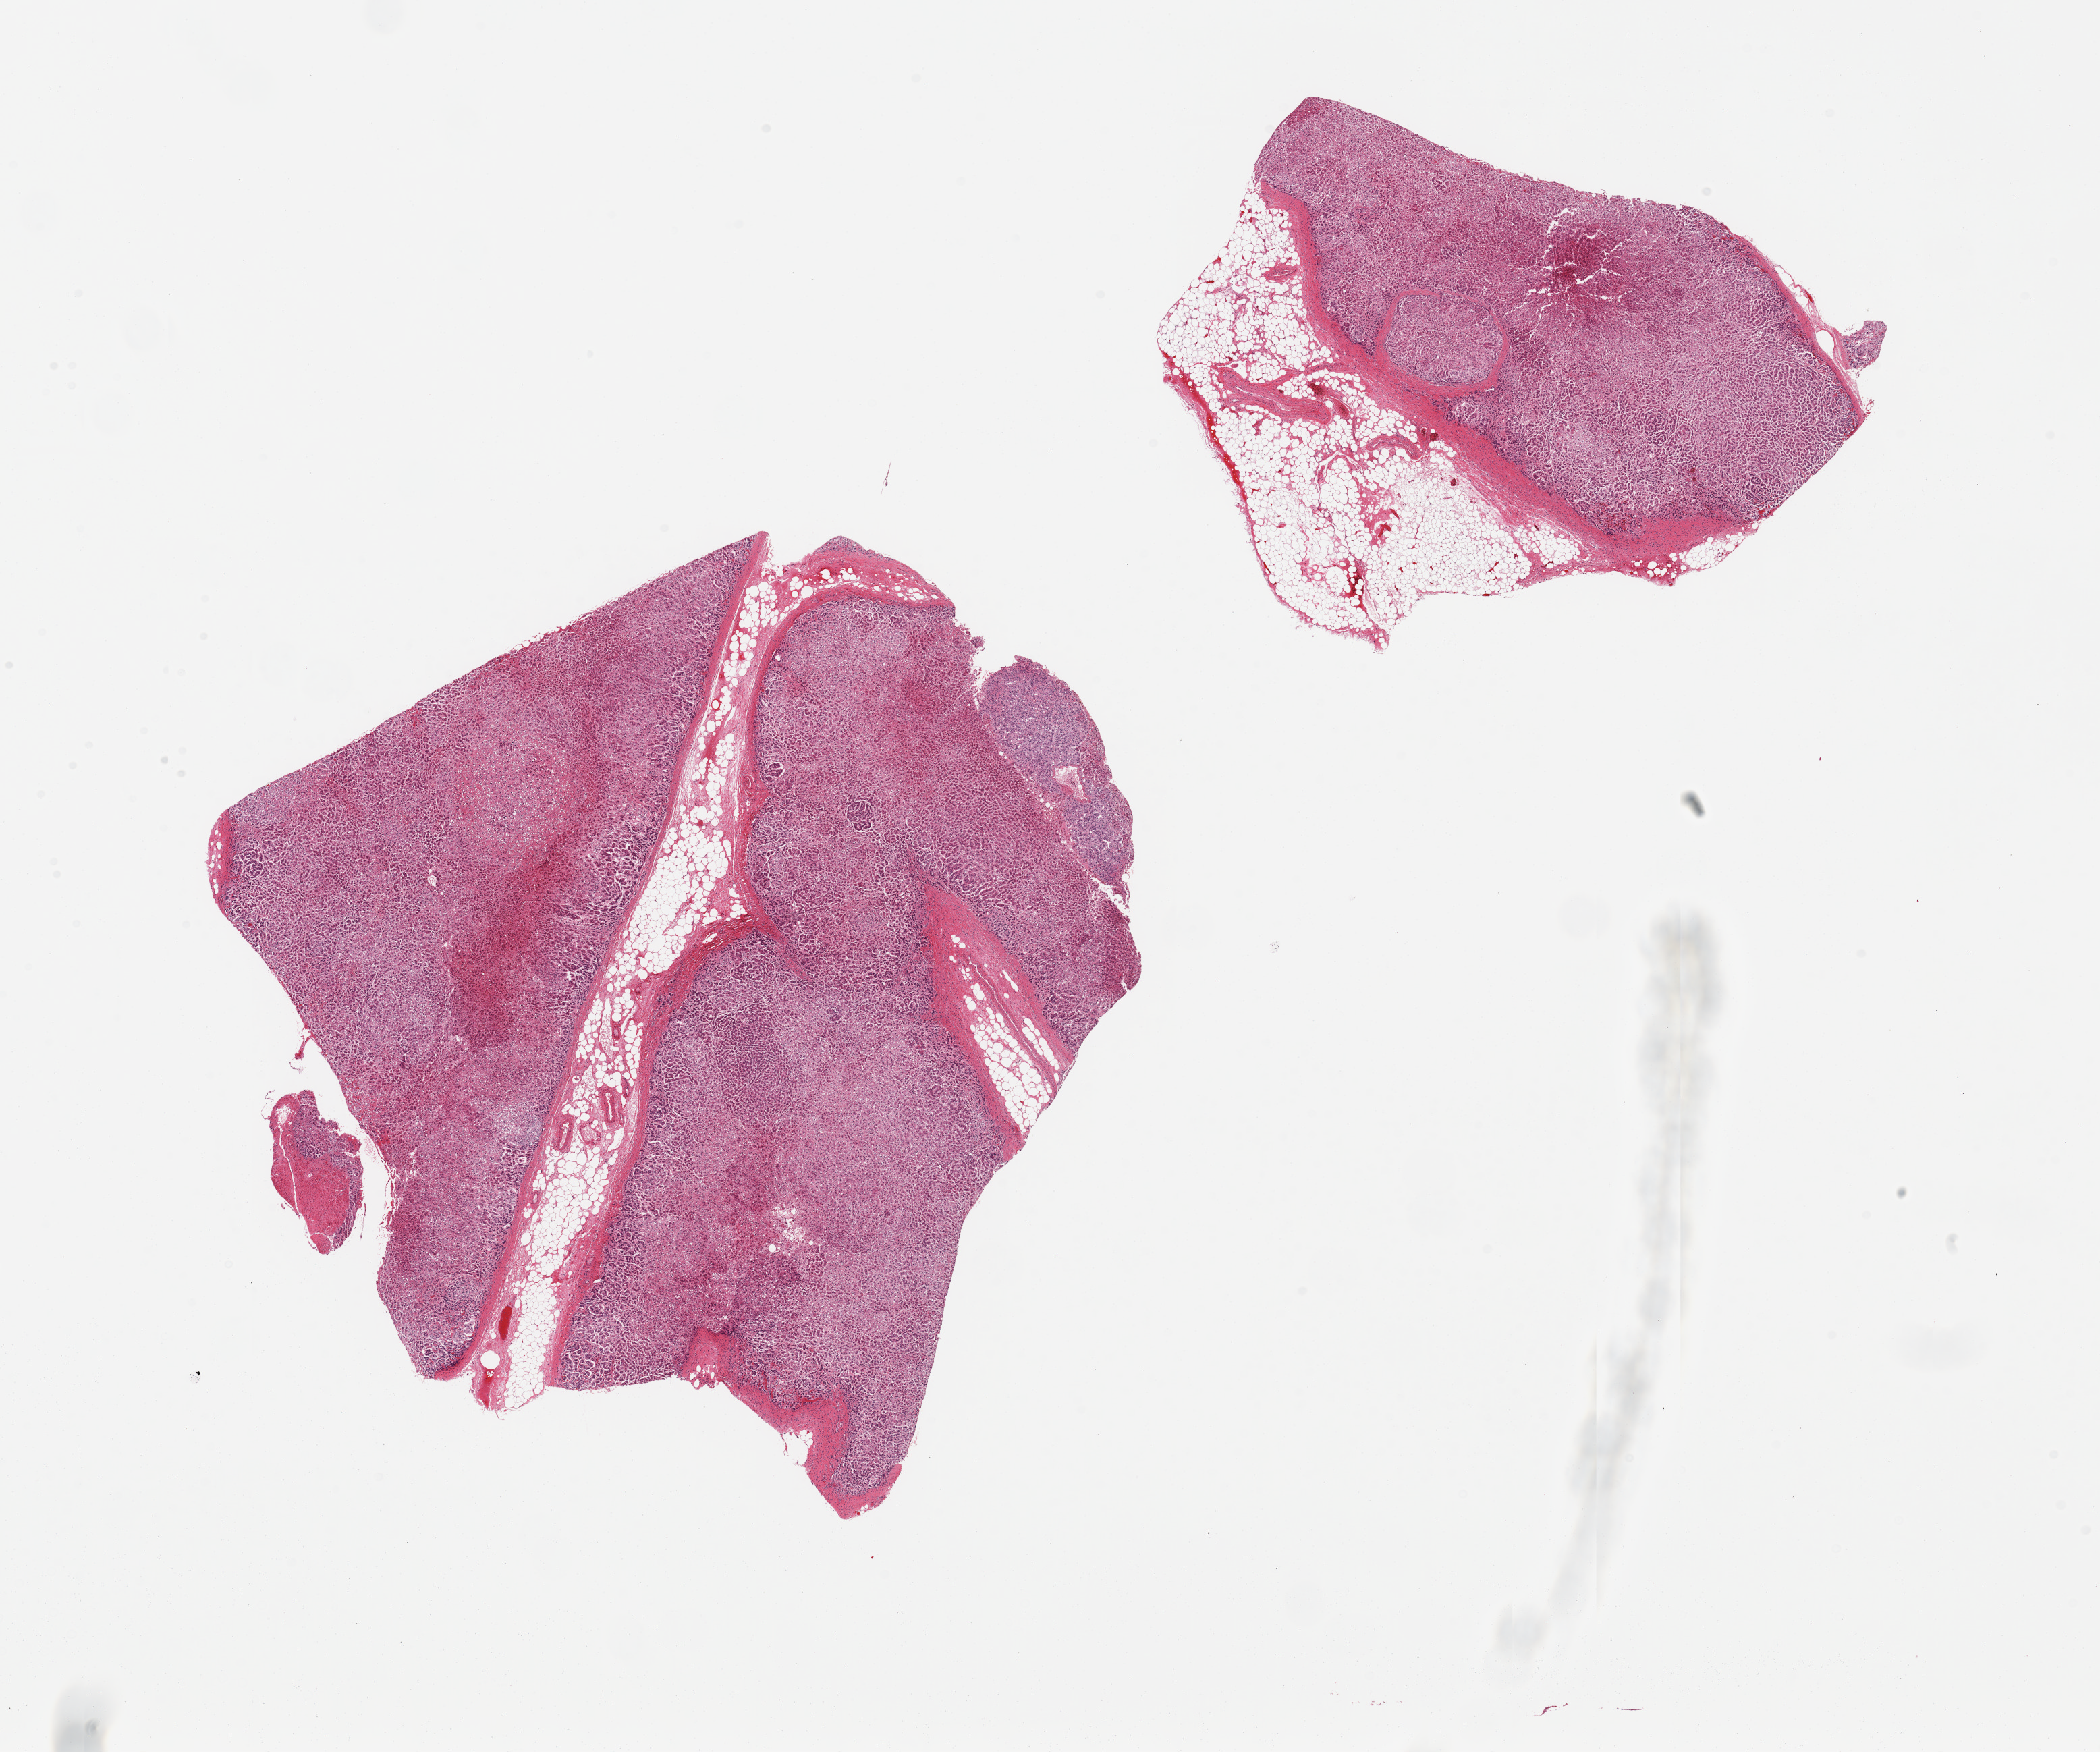
H&E whole-slide image — low-resolution overview of the scanned area, about 24.6 x 20.5 mm; PAXgene-fixed, paraffin-embedded tissue; target tissue: adrenal gland; donor tissue sample. Male donor.
Reviewer comment on this tissue sample: 2 pieces; 40% external fat in 1 piece.